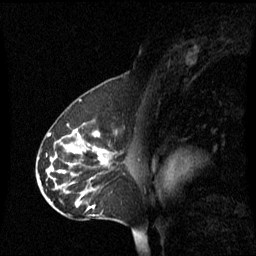
Breast MRI (dynamic contrast-enhanced), one sagittal slice. Position 37 of 60 along the scan axis. Dynamic contrast-enhanced series, image 2 of 3 at this slice position (ordered by acquisition). 1.5 T. TE 4.2 ms, TR 8.4 ms. 2.2 mm slice thickness. 256 × 256 image matrix, field of view 240 × 240 mm. Patient: female, 45 years. From the clinical record (not read from this slice): setting: breast cancer imaged before/during neoadjuvant chemotherapy; receptor status: HR-positive, HER2-negative.
Annotated regions visible in this slice (semi-automatically segmented with operator editing):
- analysis volume of interest (the breast-tissue region the enhancement analysis was run in; not a lesion): bounding box (x1, y1, x2, y2) in pixels: (38, 120, 131, 221)
- tumour enhancement mask (voxels above the 70 % enhancement threshold inside the analysis volume of interest): (50, 130, 107, 171)